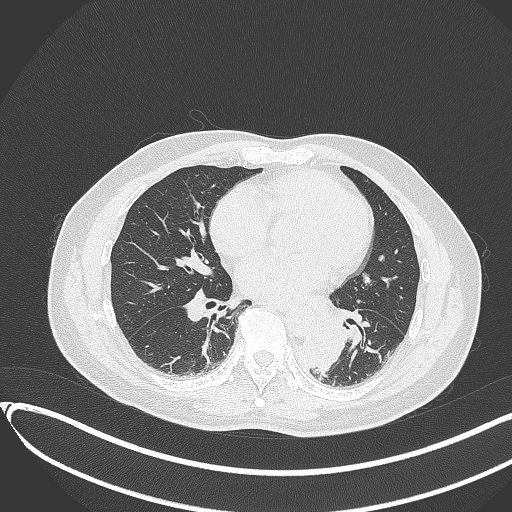
Chest CT, one axial slice. Slice 147 of 417 in the series (ordered by position). Reconstruction kernel B70f. 120 kVp. Lung window (W 1500 / L -600 HU). 1 mm slice thickness. 512 × 512 image matrix. Patient: male, 54 years. From the clinical record (not read from this slice): clinical TNM (as recorded): T3 N0 M0.
Annotated regions visible in this slice (bounding box drawn by a radiologist):
- lung tumour (recorded histology: squamous cell carcinoma): bounding box <301,326,349,372> (left, top, right, bottom; pixels)